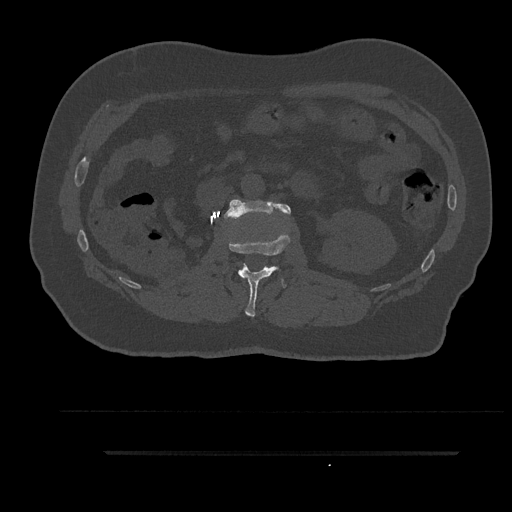
CT including the spine, one axial slice. Position 155 of 797 along the scan axis. Reconstruction kernel Br40s/3. Bone window (W 1800 / L 400 HU). 512 × 512 image matrix. Patient: male, 63 years. From the clinical record (not read from this slice): primary cancer: renal; vertebrae with lytic lesions (as recorded): T8.
Outlined on this slice (semi-automatic segmentation, software-assisted and operator-edited):
- L1 vertebra: bounding box <228,232,290,317> (left, top, right, bottom; pixels)
- L2 vertebra: <224,199,291,219>